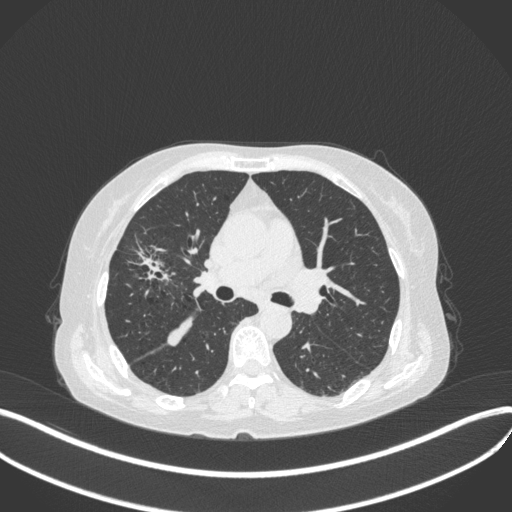
Chest CT, one axial slice. Position 237 of 429 along the scan axis. Reconstruction kernel B31f. 120 kVp. Lung window (W 1500 / L -600 HU). 512 × 512 image matrix. Patient: female, 69 years. Case-level facts recorded for this patient, not image findings: clinical TNM (as recorded): T1b N3 M0.
Structures marked on this image (bounding box drawn by a radiologist):
- lung tumour (recorded histology: small cell carcinoma): bounding box [x1, y1, x2, y2] px = [123, 242, 172, 289]